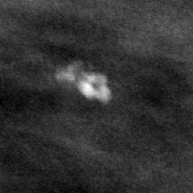
Cropped region of a digitized screen-film mammogram centred on a radiologist-marked abnormality; left breast; MLO view; BI-RADS breast density category 3 (scale 1–4).
Marked abnormality: calcifications, morphology round and regular / lucent center; BI-RADS assessment category 2; subtlety rating 5 on a 1 (subtle) to 5 (obvious) scale; benign; no additional work-up was recommended (benign without callback).